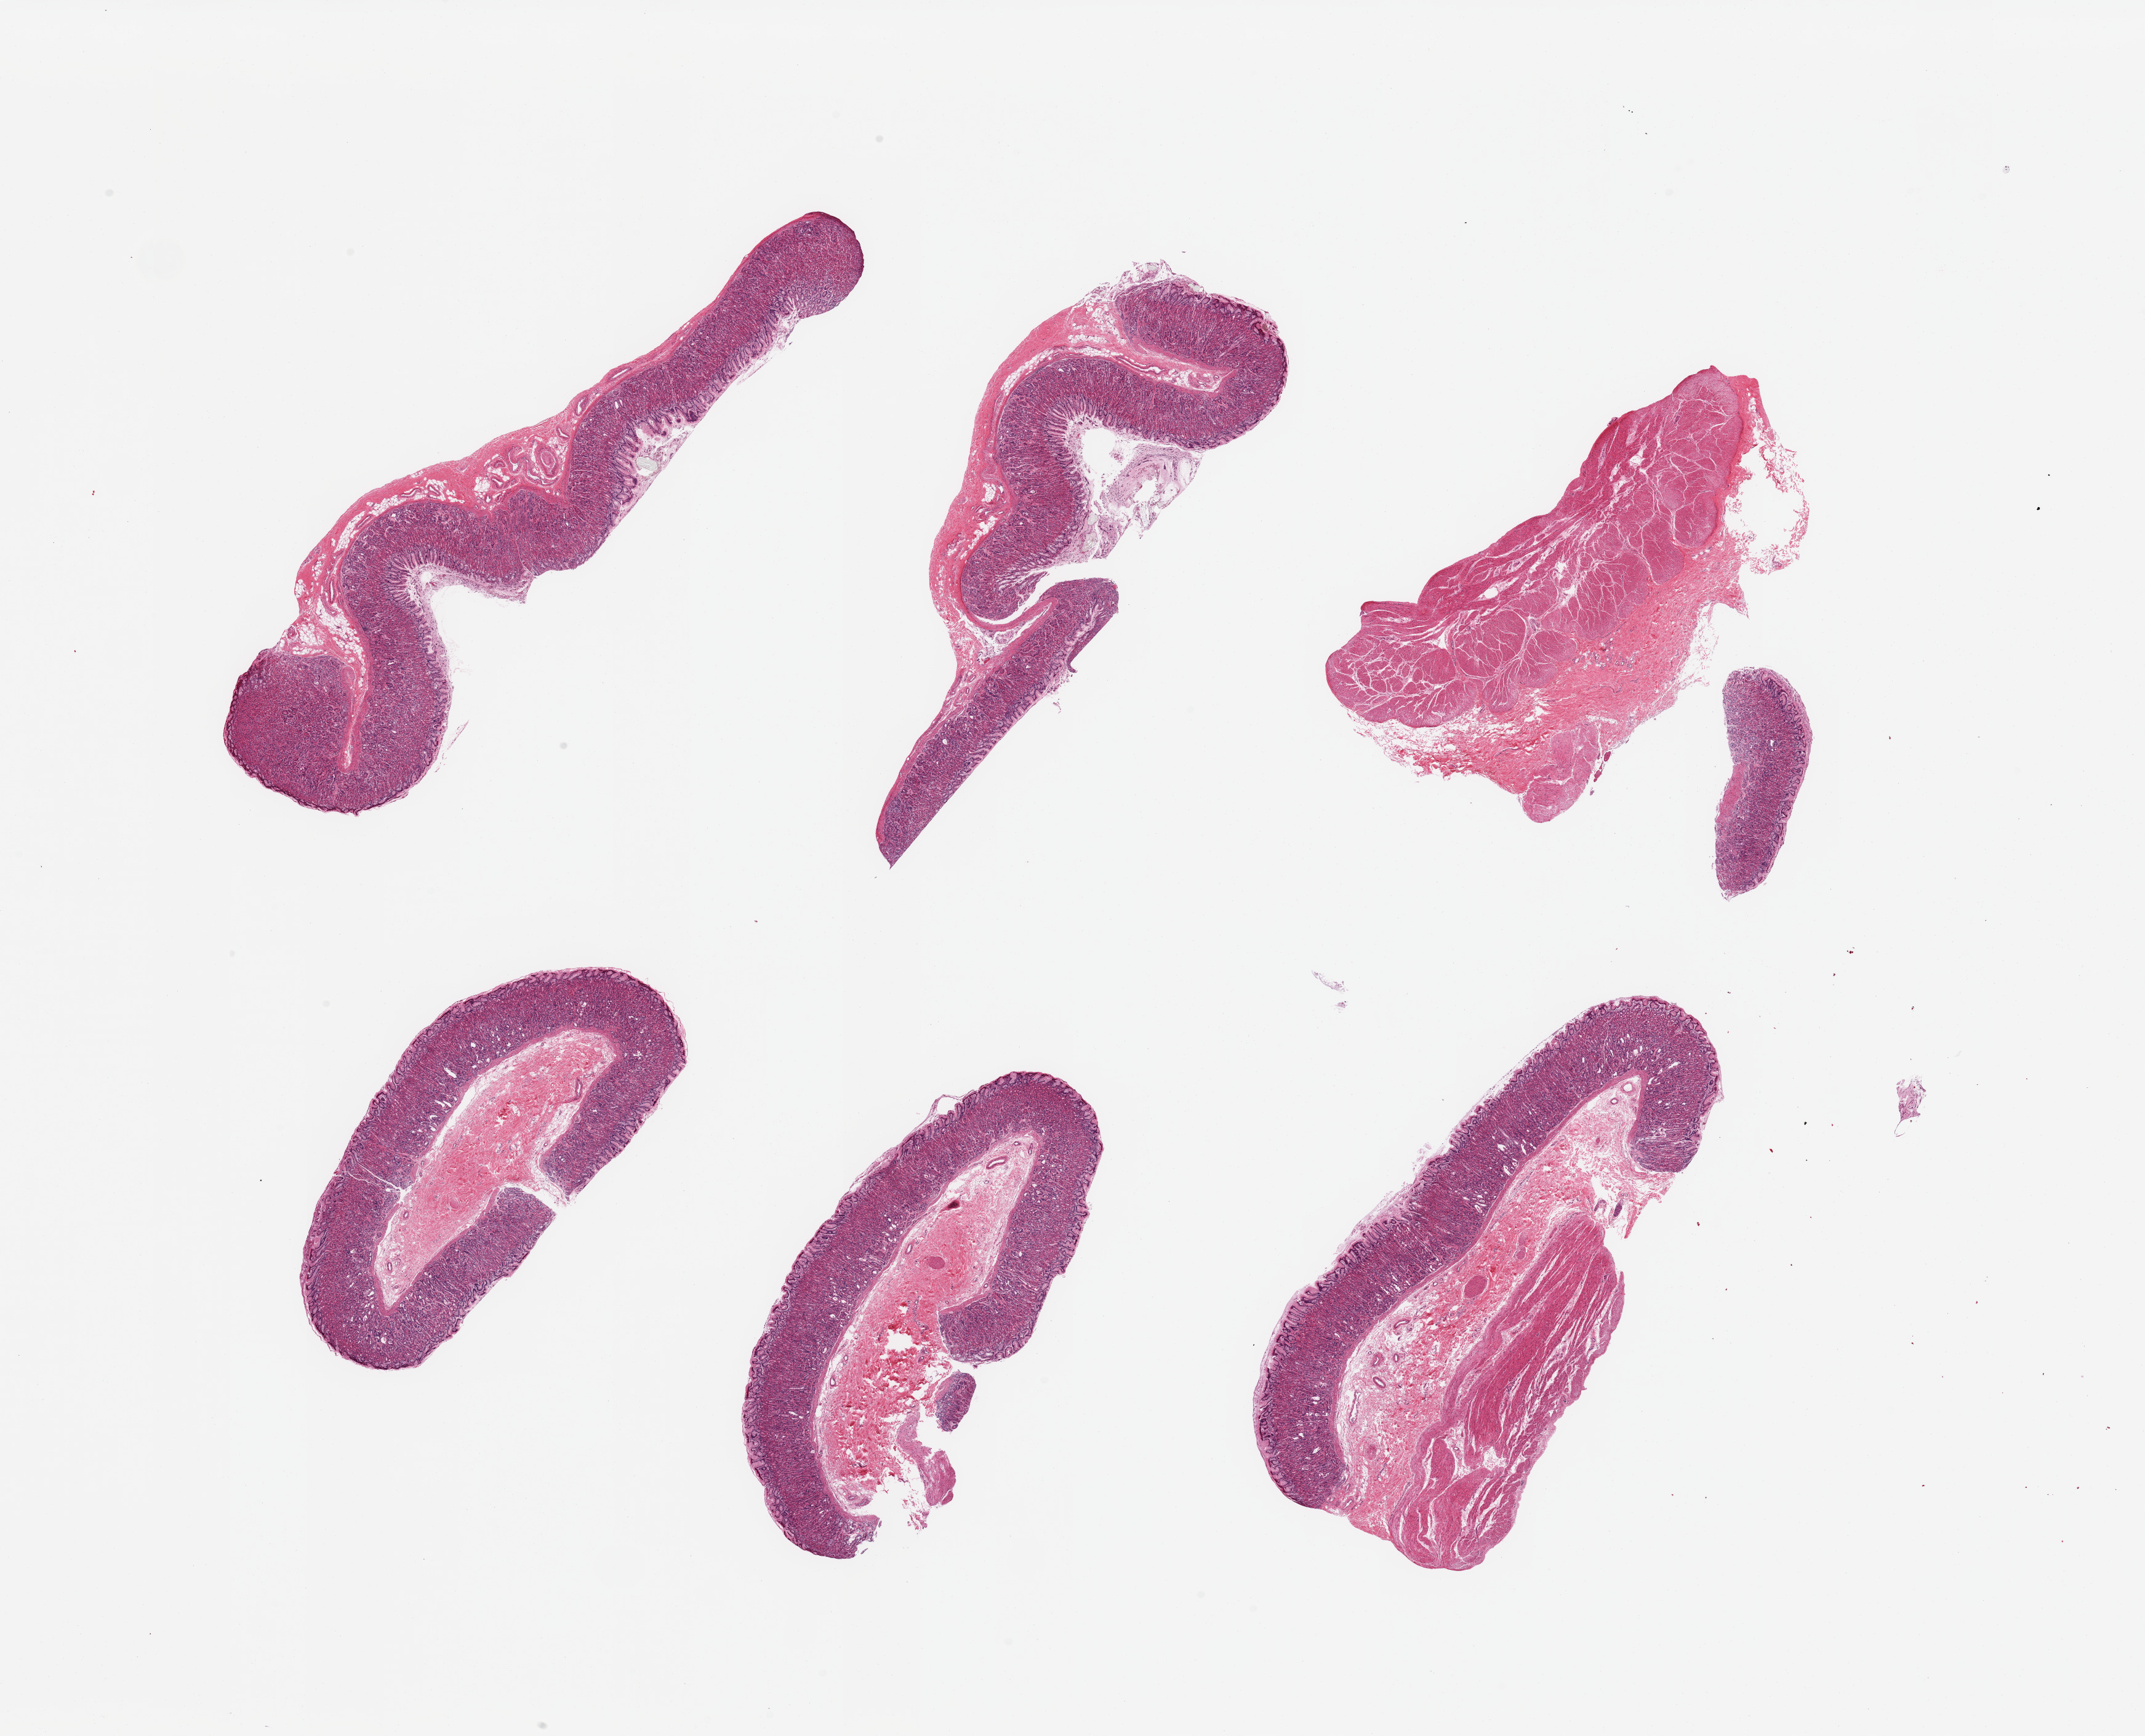
Haematoxylin and eosin whole-slide image, a low-resolution overview of the entire scanned area, about 27.6 x 22.3 mm. Female donor.
Specimen: PAXgene-fixed, paraffin-embedded tissue; target tissue: stomach; donor tissue sample.